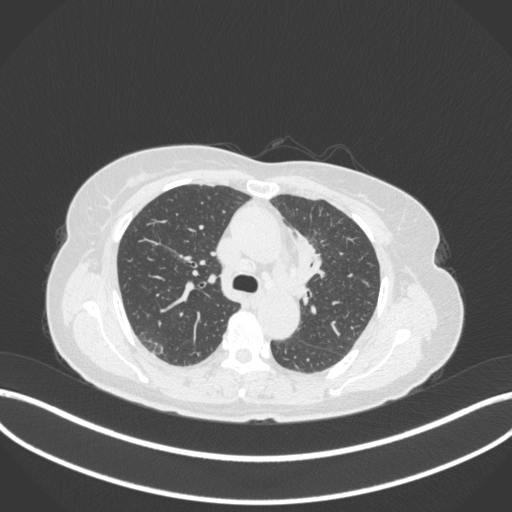
Chest CT, one axial slice; slice 226 of 368 in the series (ordered by position); reconstruction kernel B31f; lung window (W 1500 / L -600 HU); 1 mm slice thickness; 512 × 512 image matrix, field of view 400 × 400 mm. Female patient, age 65 years. From the clinical record (not read from this slice): clinical TNM (as recorded): T2a N0 M0; histopathological grade: G2-3.
Annotated regions visible in this slice (bounding box drawn by a radiologist):
- lung tumour (recorded histology: adenocarcinoma): bounding box <293,230,326,283> (left, top, right, bottom; pixels)